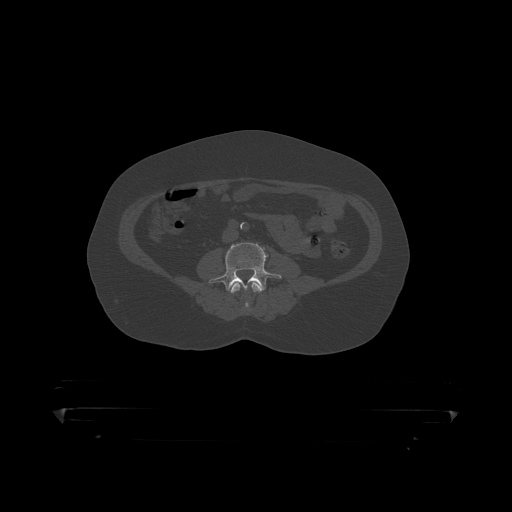
CT including the spine, one axial slice; slice 71 of 390 in the series (ordered by position); reconstruction kernel STANDARD; 120 kVp; bone window (W 1800 / L 400 HU); 1.25 mm slice thickness; 512 × 512 image matrix. Male patient, age 60 years. From the clinical record (not read from this slice): primary cancer: prostate.
Structures marked on this image (semi-automatically segmented with operator editing):
- L3 vertebra: box from (x=230, y=280) to (x=264, y=311) px
- L4 vertebra: (x=209, y=241)–(x=282, y=292)